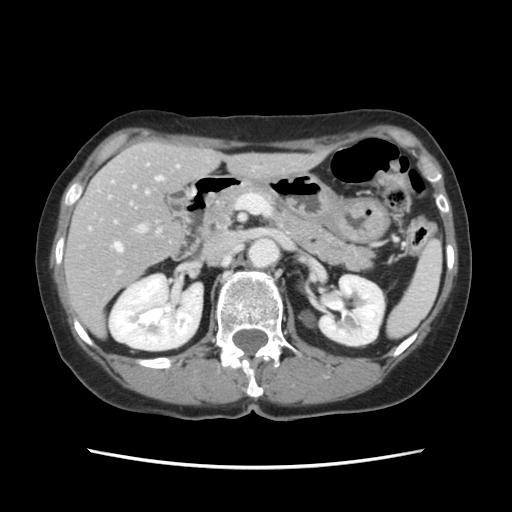
Contrast-enhanced abdominal CT, one axial slice. Position 64 of 120 along the scan axis. 120 kVp. Intravenous contrast given. Soft-tissue window (W 400 / L 40 HU). 2.5 mm slice thickness. 512 × 512 image matrix, field of view 330 × 330 mm. Female patient, age 70 years. Case-level facts recorded for this patient, not image findings: diagnosis: colorectal cancer liver metastases, imaged before liver resection; multiple liver metastases: no; largest metastasis: 2.5 cm; disease in both lobes: no.
Annotated regions visible in this slice (outlined manually by an expert reader):
- hepatic veins: bounding box (x1, y1, x2, y2) in pixels: (114, 165, 163, 252)
- liver: (66, 143, 320, 333)
- planned liver remnant (the part of the liver to remain after resection): (76, 143, 321, 279)
- portal vein (with intrahepatic branches): (108, 166, 179, 233)